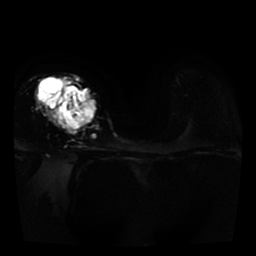
Breast MRI, one axial slice. Position 26 of 41 along the scan axis. Diffusion-weighted series; image 2 of 4 stored at this slice position (different b-values; order by instance number). 1.5 T. 256 × 256 image matrix, field of view 330 × 330 mm. Female patient.
Annotated regions visible in this slice (expert manual segmentation):
- tumour on diffusion-weighted imaging: bounding box [x1, y1, x2, y2] px = [46, 80, 95, 133]